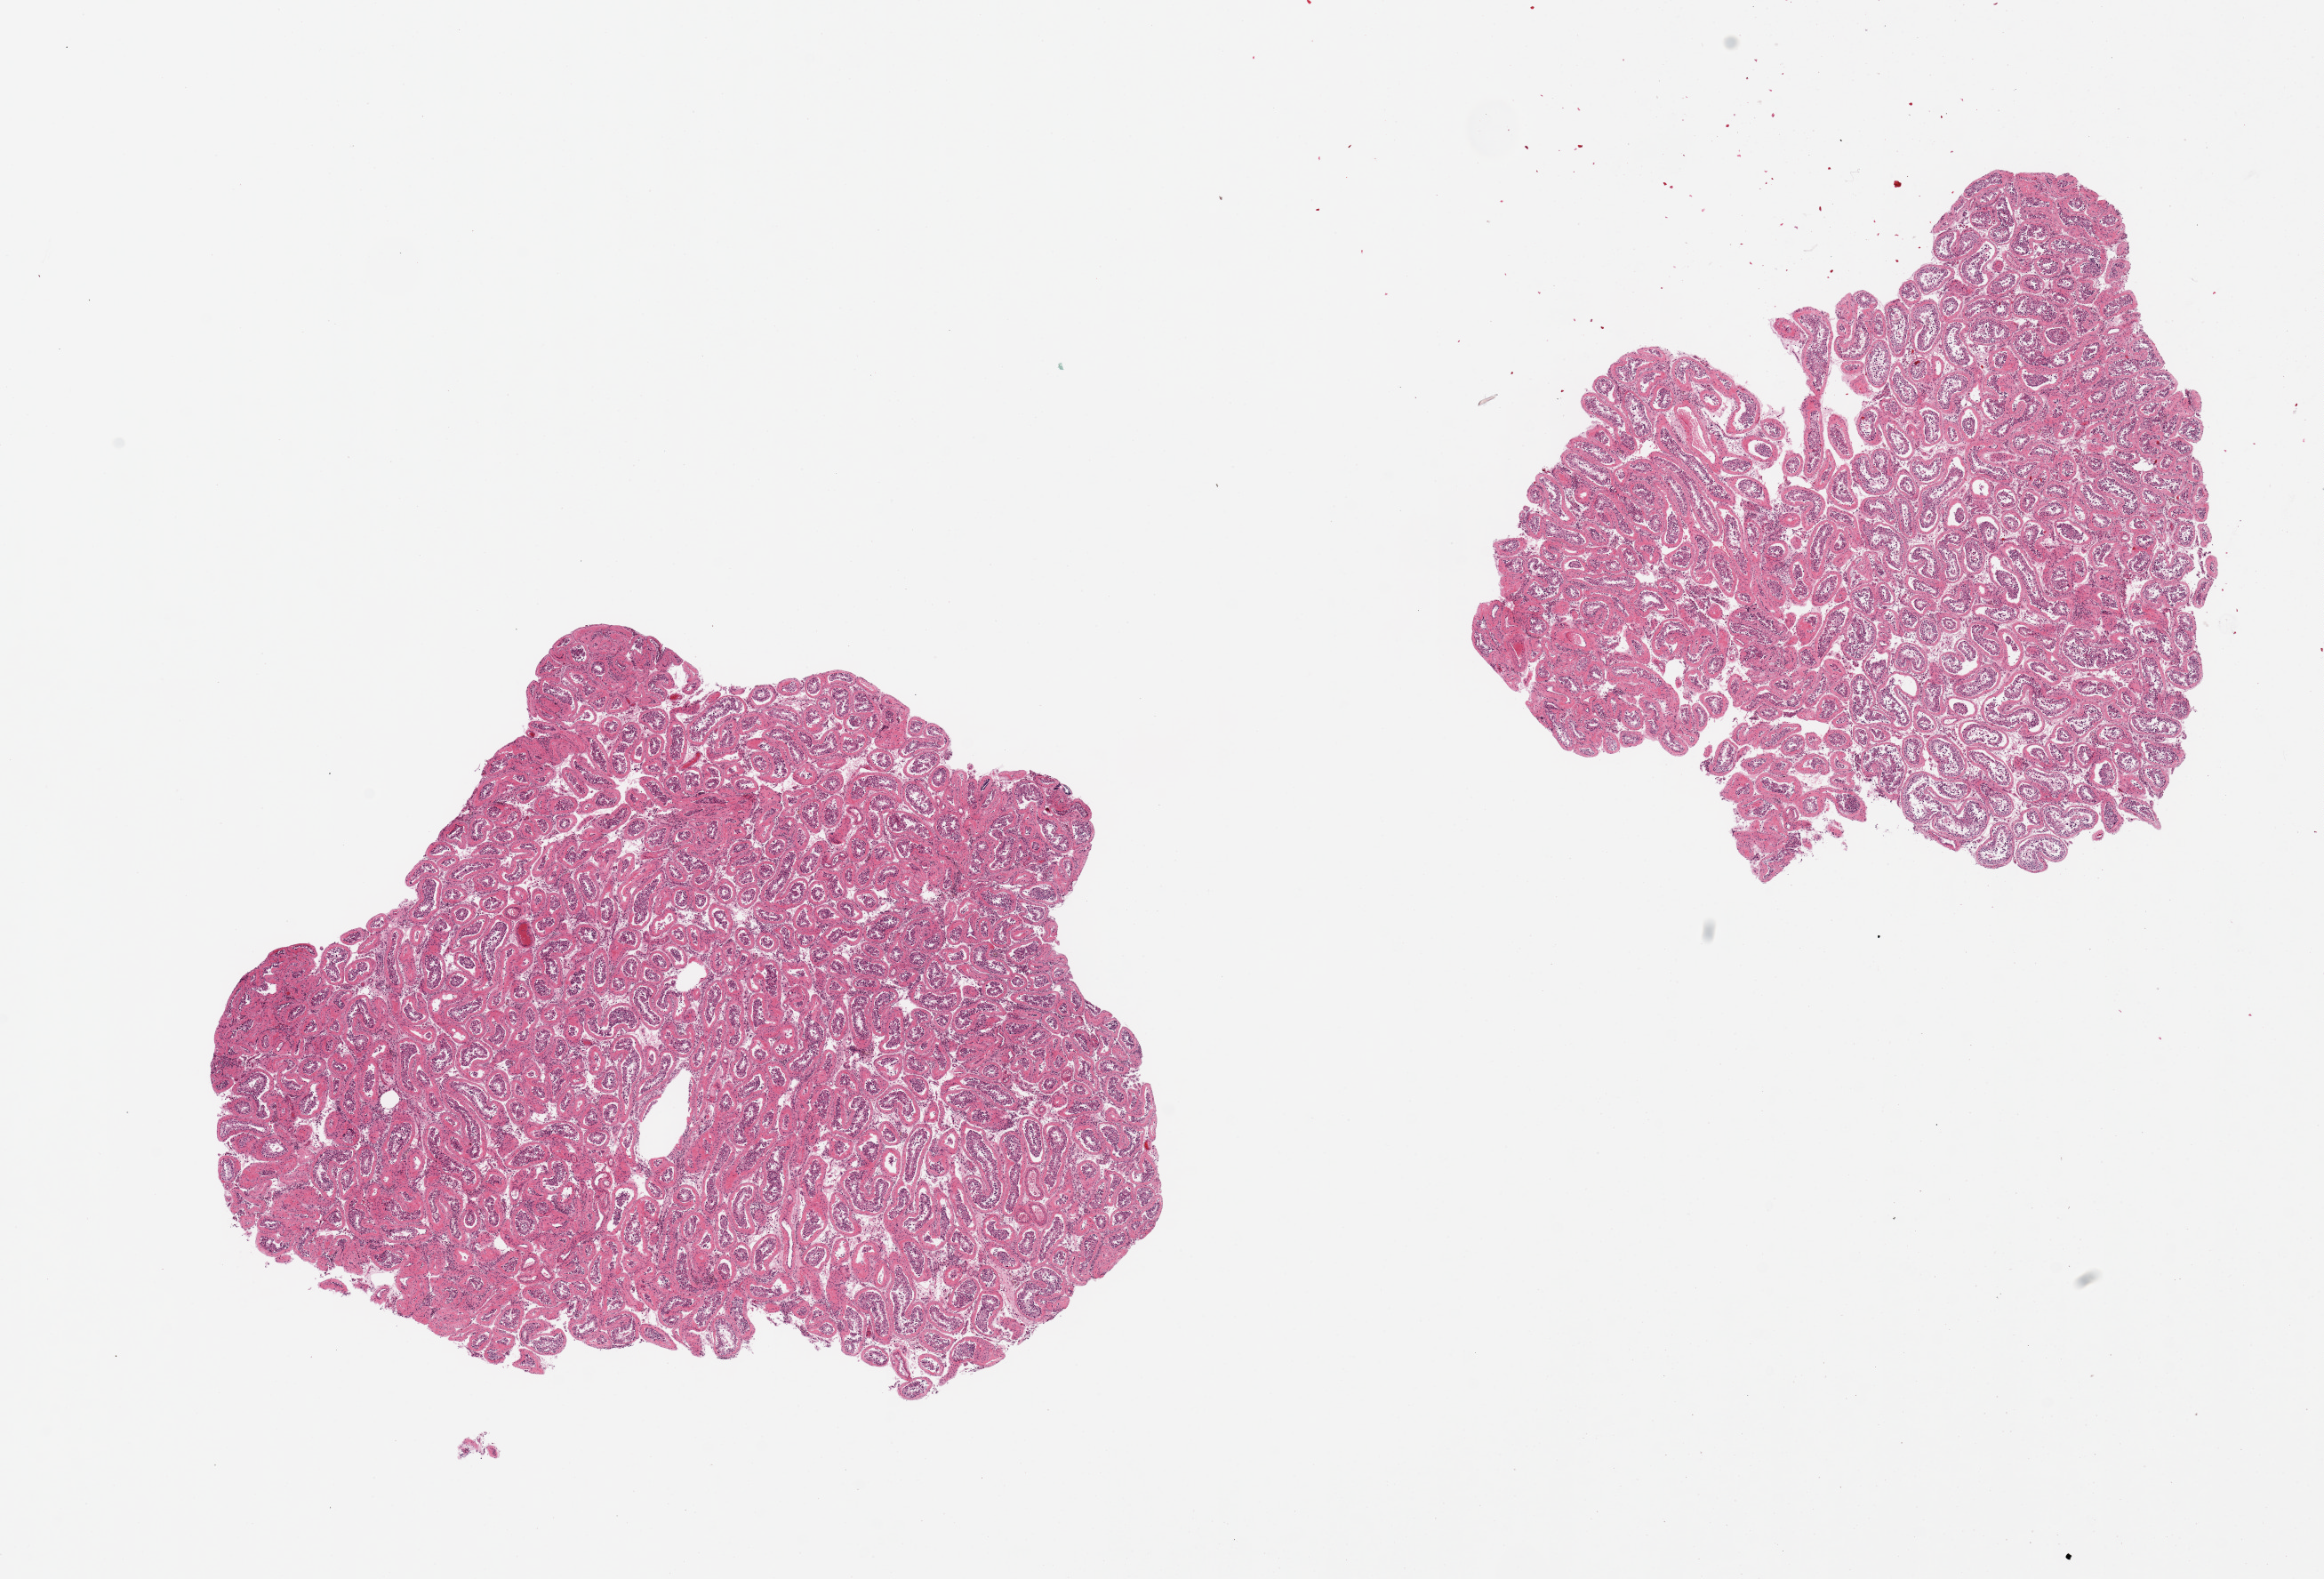
Whole-slide image, haematoxylin and eosin stain — shown as a low-resolution overview of the whole scanned area (about 20.7 x 14.0 mm), PAXgene-fixed paraffin-embedded (PFPE) section, section of testis (target tissue), donor tissue sample. Male donor.
Review note (as recorded): 2 pieces, decreased spermatogenesis and peritubular fibrosis.